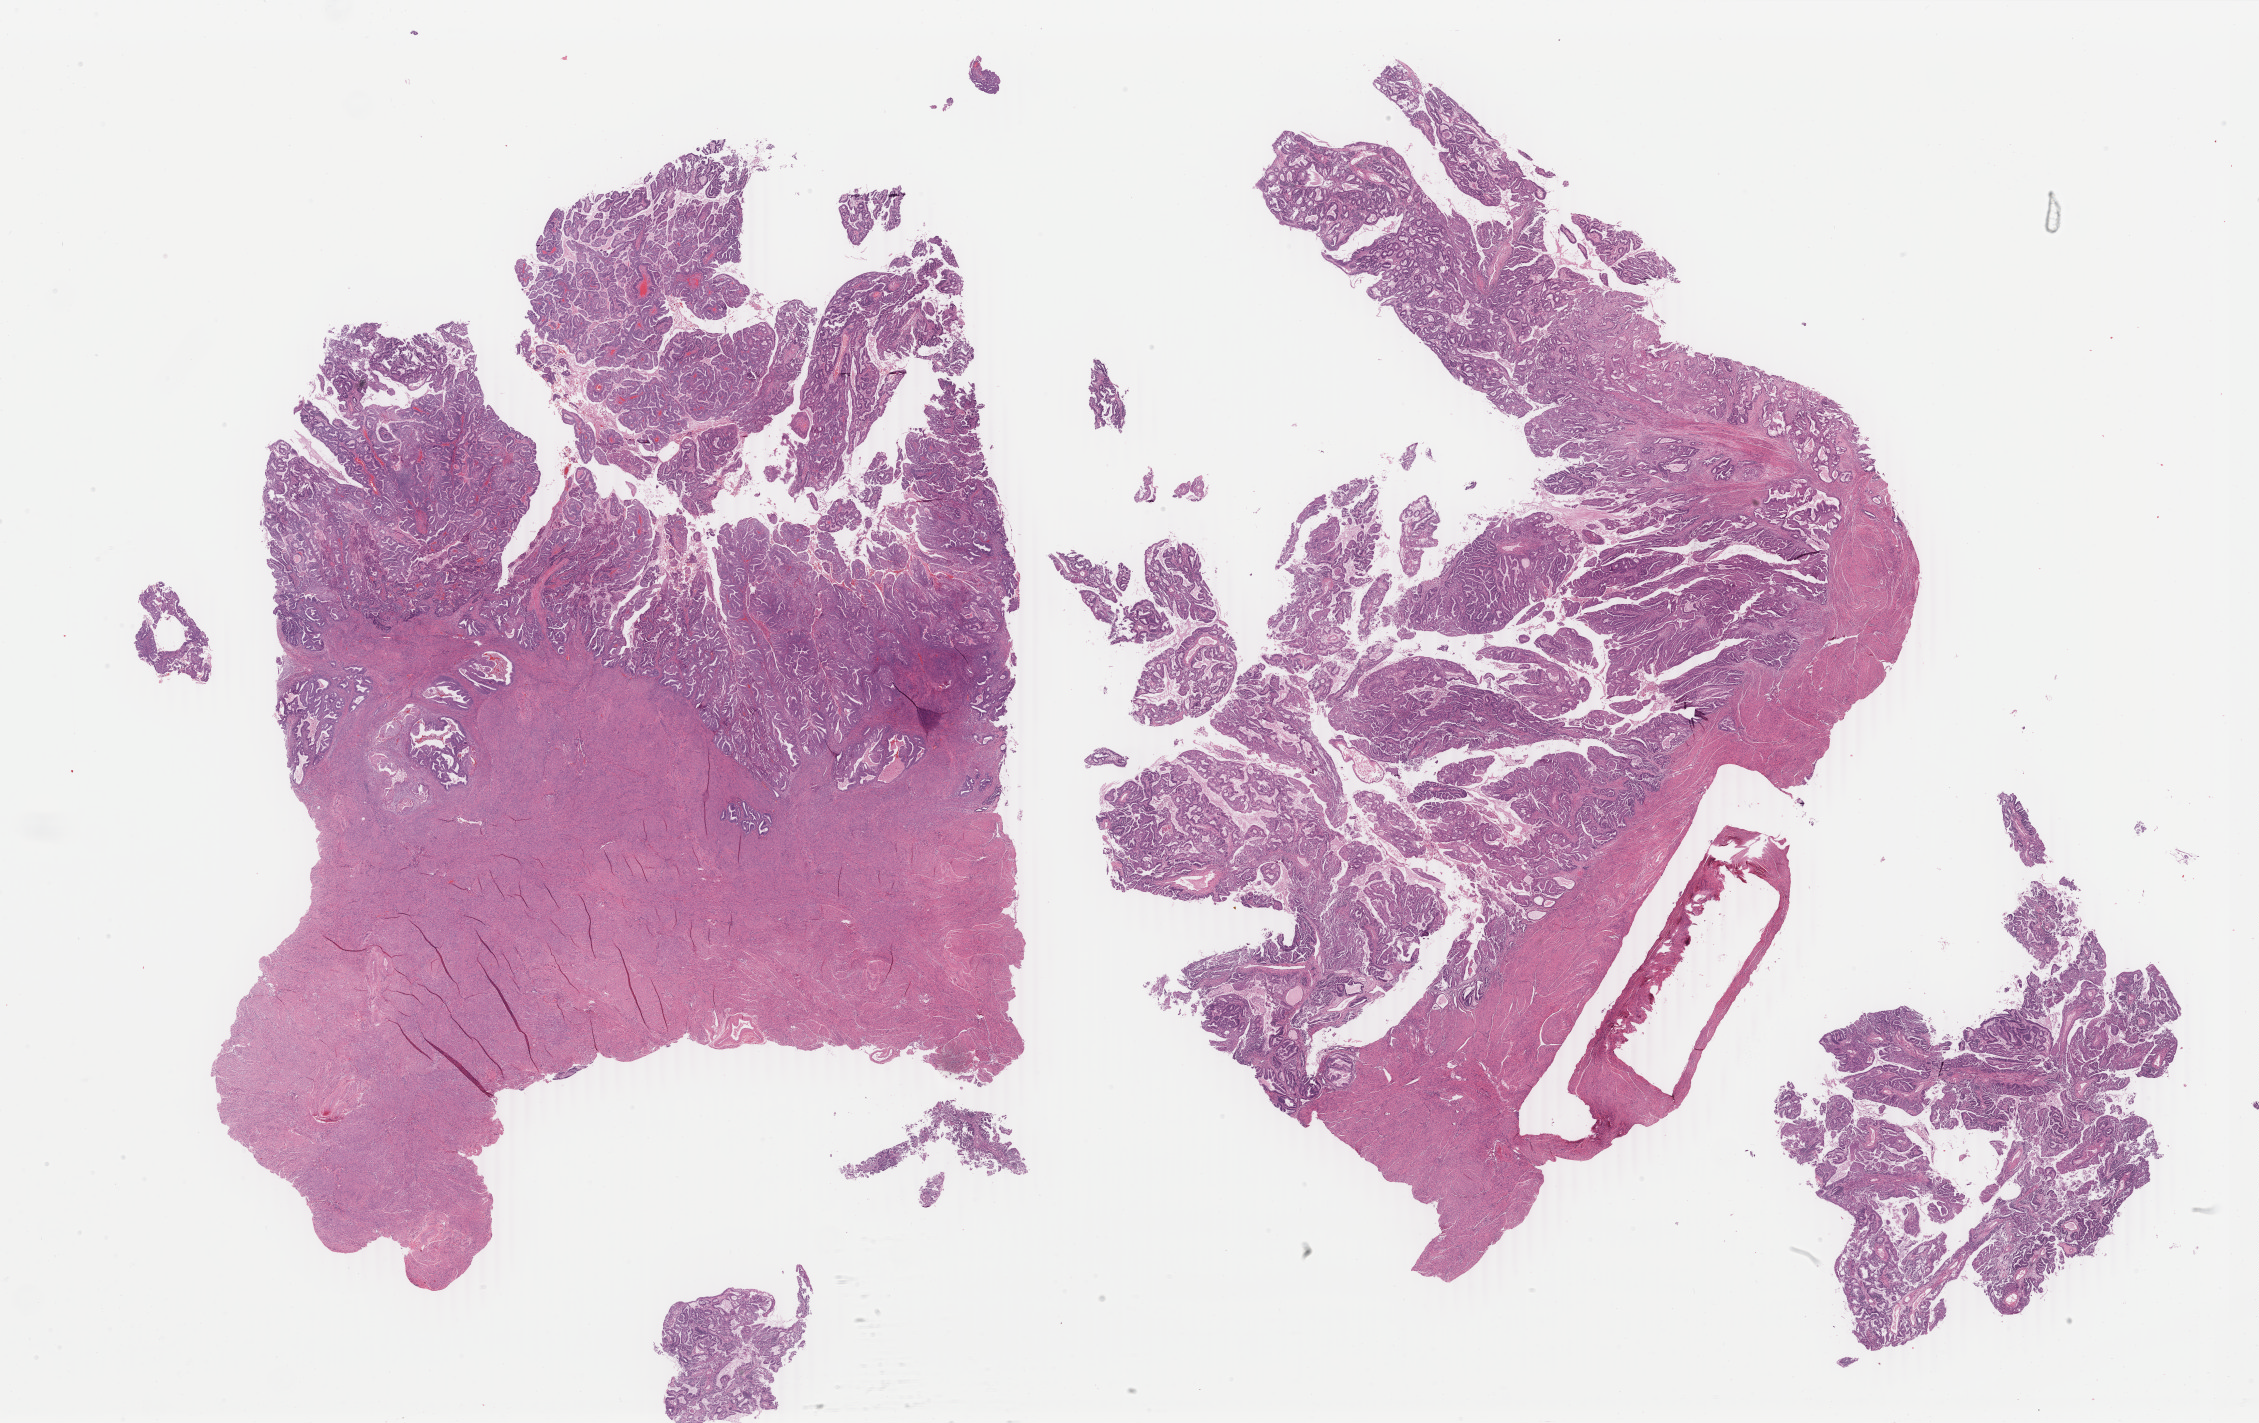
H&E whole-slide image — whole scanned area (about 35.9 x 22.6 mm, acquisition: 40x scan) shown as a low-resolution overview; formalin-fixed paraffin-embedded (FFPE) diagnostic section; primary tumour sample from the uterus. Patient: female, age at initial diagnosis 56 years.
Pathologic diagnosis: Endometrioid adenocarcinoma, NOS (endometrium).